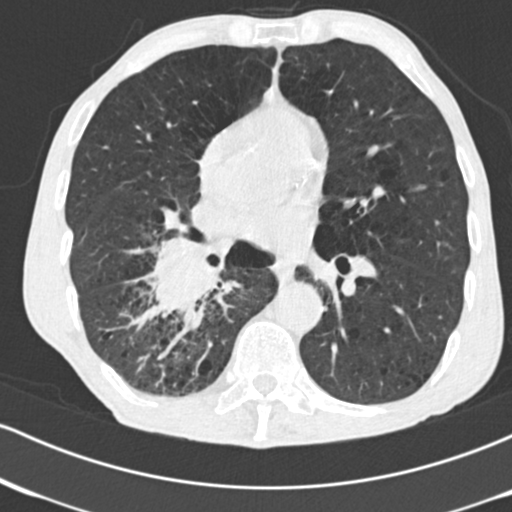
Low-dose screening chest CT, one axial slice. Slice 81 of 182 in the series (ordered by position). Reconstruction kernel B30f. 120 kVp. Lung window (W 1500 / L -600 HU). 2 mm slice thickness. 512 × 512 image matrix, field of view 316 × 316 mm.
Outlined on this slice (outlined manually by an expert reader):
- lesion 1 (tumor, lower lobe of right lung): bounding box <150,242,220,312> (left, top, right, bottom; pixels)